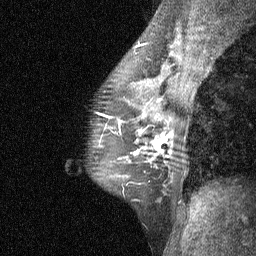
Breast MRI (dynamic contrast-enhanced), one sagittal slice; slice 41 of 64 in the series (ordered by position); dynamic contrast-enhanced study with each time point stored as its own series, time point 3 of 4 at this slice position (ordered by acquisition time); 1.5 T; TE 4.8 ms, TR 27 ms; 256 × 256 image matrix. Female patient, age 44 years. From the clinical record (not read from this slice): setting: breast cancer imaged before/during neoadjuvant chemotherapy; receptor status: HR-positive, HER2-negative.
Outlined on this slice (semi-automatic segmentation, software-assisted and operator-edited):
- analysis volume of interest (the breast-tissue region the enhancement analysis was run in; not a lesion): box from (x=115, y=117) to (x=185, y=188) px
- tumour enhancement mask (voxels above the 90 % enhancement threshold inside the analysis volume of interest): (x=119, y=118)–(x=173, y=155)